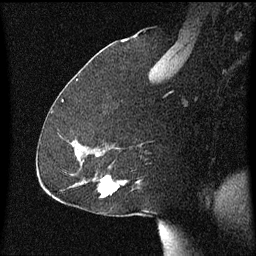
Breast MRI (dynamic contrast-enhanced), one sagittal slice. Dynamic contrast-enhanced series, image 2 of 3 at this slice position (ordered by acquisition). 1.5 T. TE 4.2 ms, TR 8.4 ms. 2 mm slice thickness. 256 × 256 image matrix, field of view 200 × 200 mm. Patient: female, 59 years.
Annotated regions visible in this slice (semi-automatic segmentation, software-assisted and operator-edited):
- analysis volume of interest (the breast-tissue region the enhancement analysis was run in; not a lesion): bounding box <94,166,139,199> (left, top, right, bottom; pixels)
- tumour enhancement mask (voxels above the 70 % enhancement threshold inside the analysis volume of interest): <98,176,119,197>